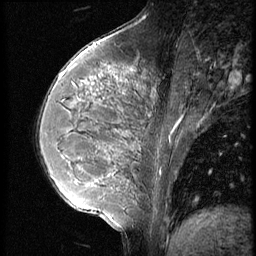
Breast MRI (dynamic contrast-enhanced), one sagittal slice; slice 22 of 56 in the series (ordered by position); 3 images stored at this slice position (order not interpretable as contrast timing); 1.5 T; TE 4.2 ms, TR 9 ms; 2.5 mm slice thickness; 256 × 256 image matrix, field of view 180 × 180 mm. Patient: female, 35 years. From the clinical record (not read from this slice): setting: breast cancer imaged before/during neoadjuvant chemotherapy; receptor status: HR-positive, HER2-negative.
Annotated regions visible in this slice (semi-automatic segmentation, software-assisted and operator-edited):
- analysis volume of interest (the breast-tissue region the enhancement analysis was run in; not a lesion): bounding box <63,60,190,218> (left, top, right, bottom; pixels)
- tumour enhancement mask (voxels above the 140 % enhancement threshold inside the analysis volume of interest): <63,71,170,187>